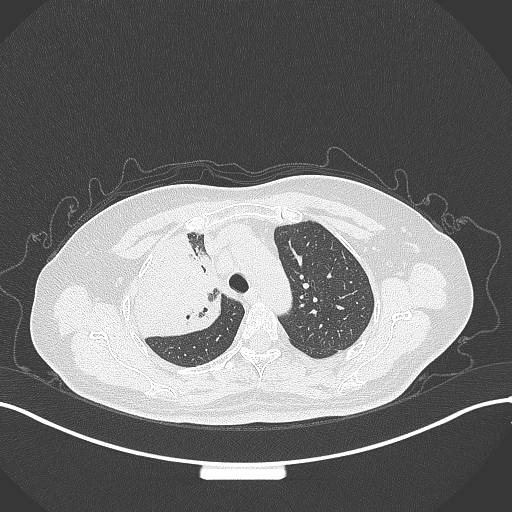
Chest CT, one axial slice; slice 238 of 309 in the series (ordered by position); lung window (W 1500 / L -600 HU); 1 mm slice thickness; 512 × 512 image matrix. Patient: female, 60 years. Case-level facts recorded for this patient, not image findings: clinical TNM (as recorded): T3 N1 M1.
Outlined on this slice (rectangle marked by the reading radiologist):
- lung tumour (recorded histology: adenocarcinoma): box from (x=130, y=228) to (x=226, y=341) px